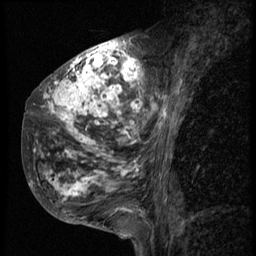
Breast MRI (dynamic contrast-enhanced), one sagittal slice. Slice 22 of 58 in the series (ordered by position). 3 images stored at this slice position (order not interpretable as contrast timing). 1.5 T. TE 4.2 ms, TR 9 ms. 2.5 mm slice thickness. 256 × 256 image matrix, field of view 180 × 180 mm. Female patient, age 50 years. From the clinical record (not read from this slice): setting: breast cancer imaged before/during neoadjuvant chemotherapy; receptor status: triple-negative.
Annotated regions visible in this slice (semi-automatic segmentation, software-assisted and operator-edited):
- analysis volume of interest (the breast-tissue region the enhancement analysis was run in; not a lesion): bounding box <23,48,177,214> (left, top, right, bottom; pixels)
- tumour enhancement mask (voxels above the 140 % enhancement threshold inside the analysis volume of interest): <30,48,177,212>